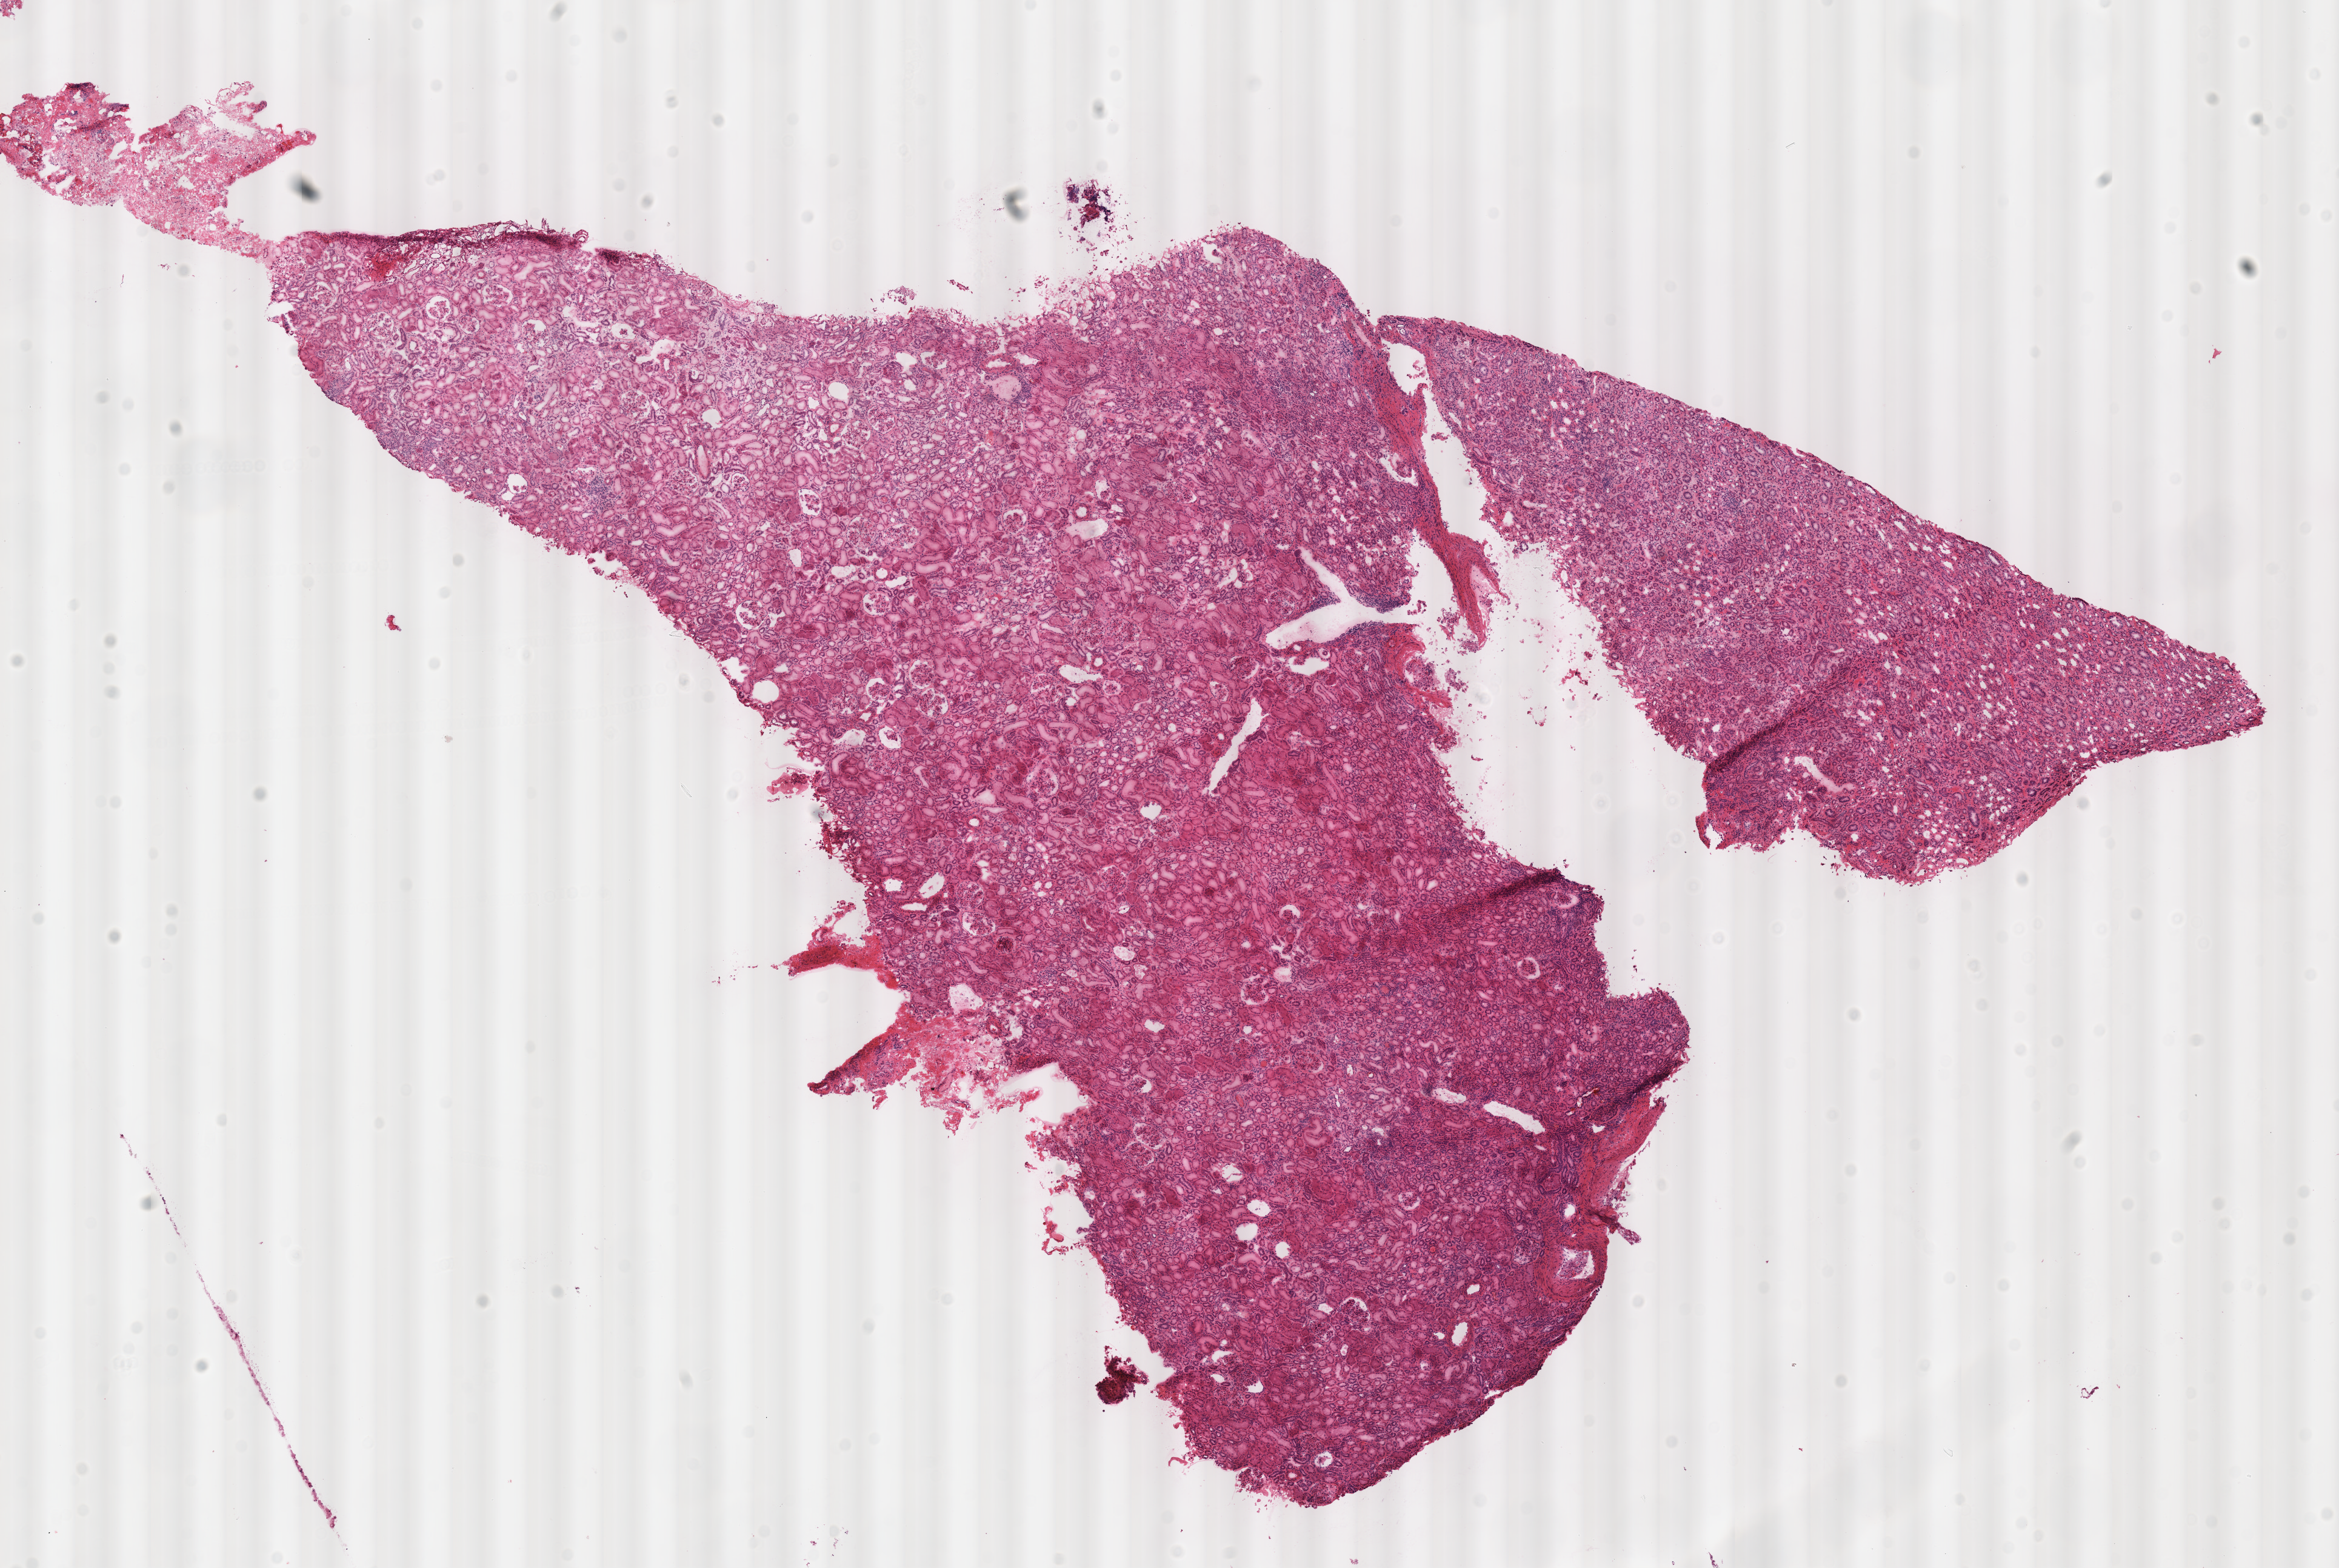
H&E-stained whole-slide image, whole scanned area (about 15.2 x 10.2 mm) shown as a low-resolution overview; frozen section from the top of the tissue portion; kidney, solid tissue normal (non-tumour tissue) sample. Female, age 45 years at initial diagnosis.
This section: solid tissue normal (non-tumour) sample from the same patient. Patient diagnosis: Renal cell carcinoma, chromophobe type.